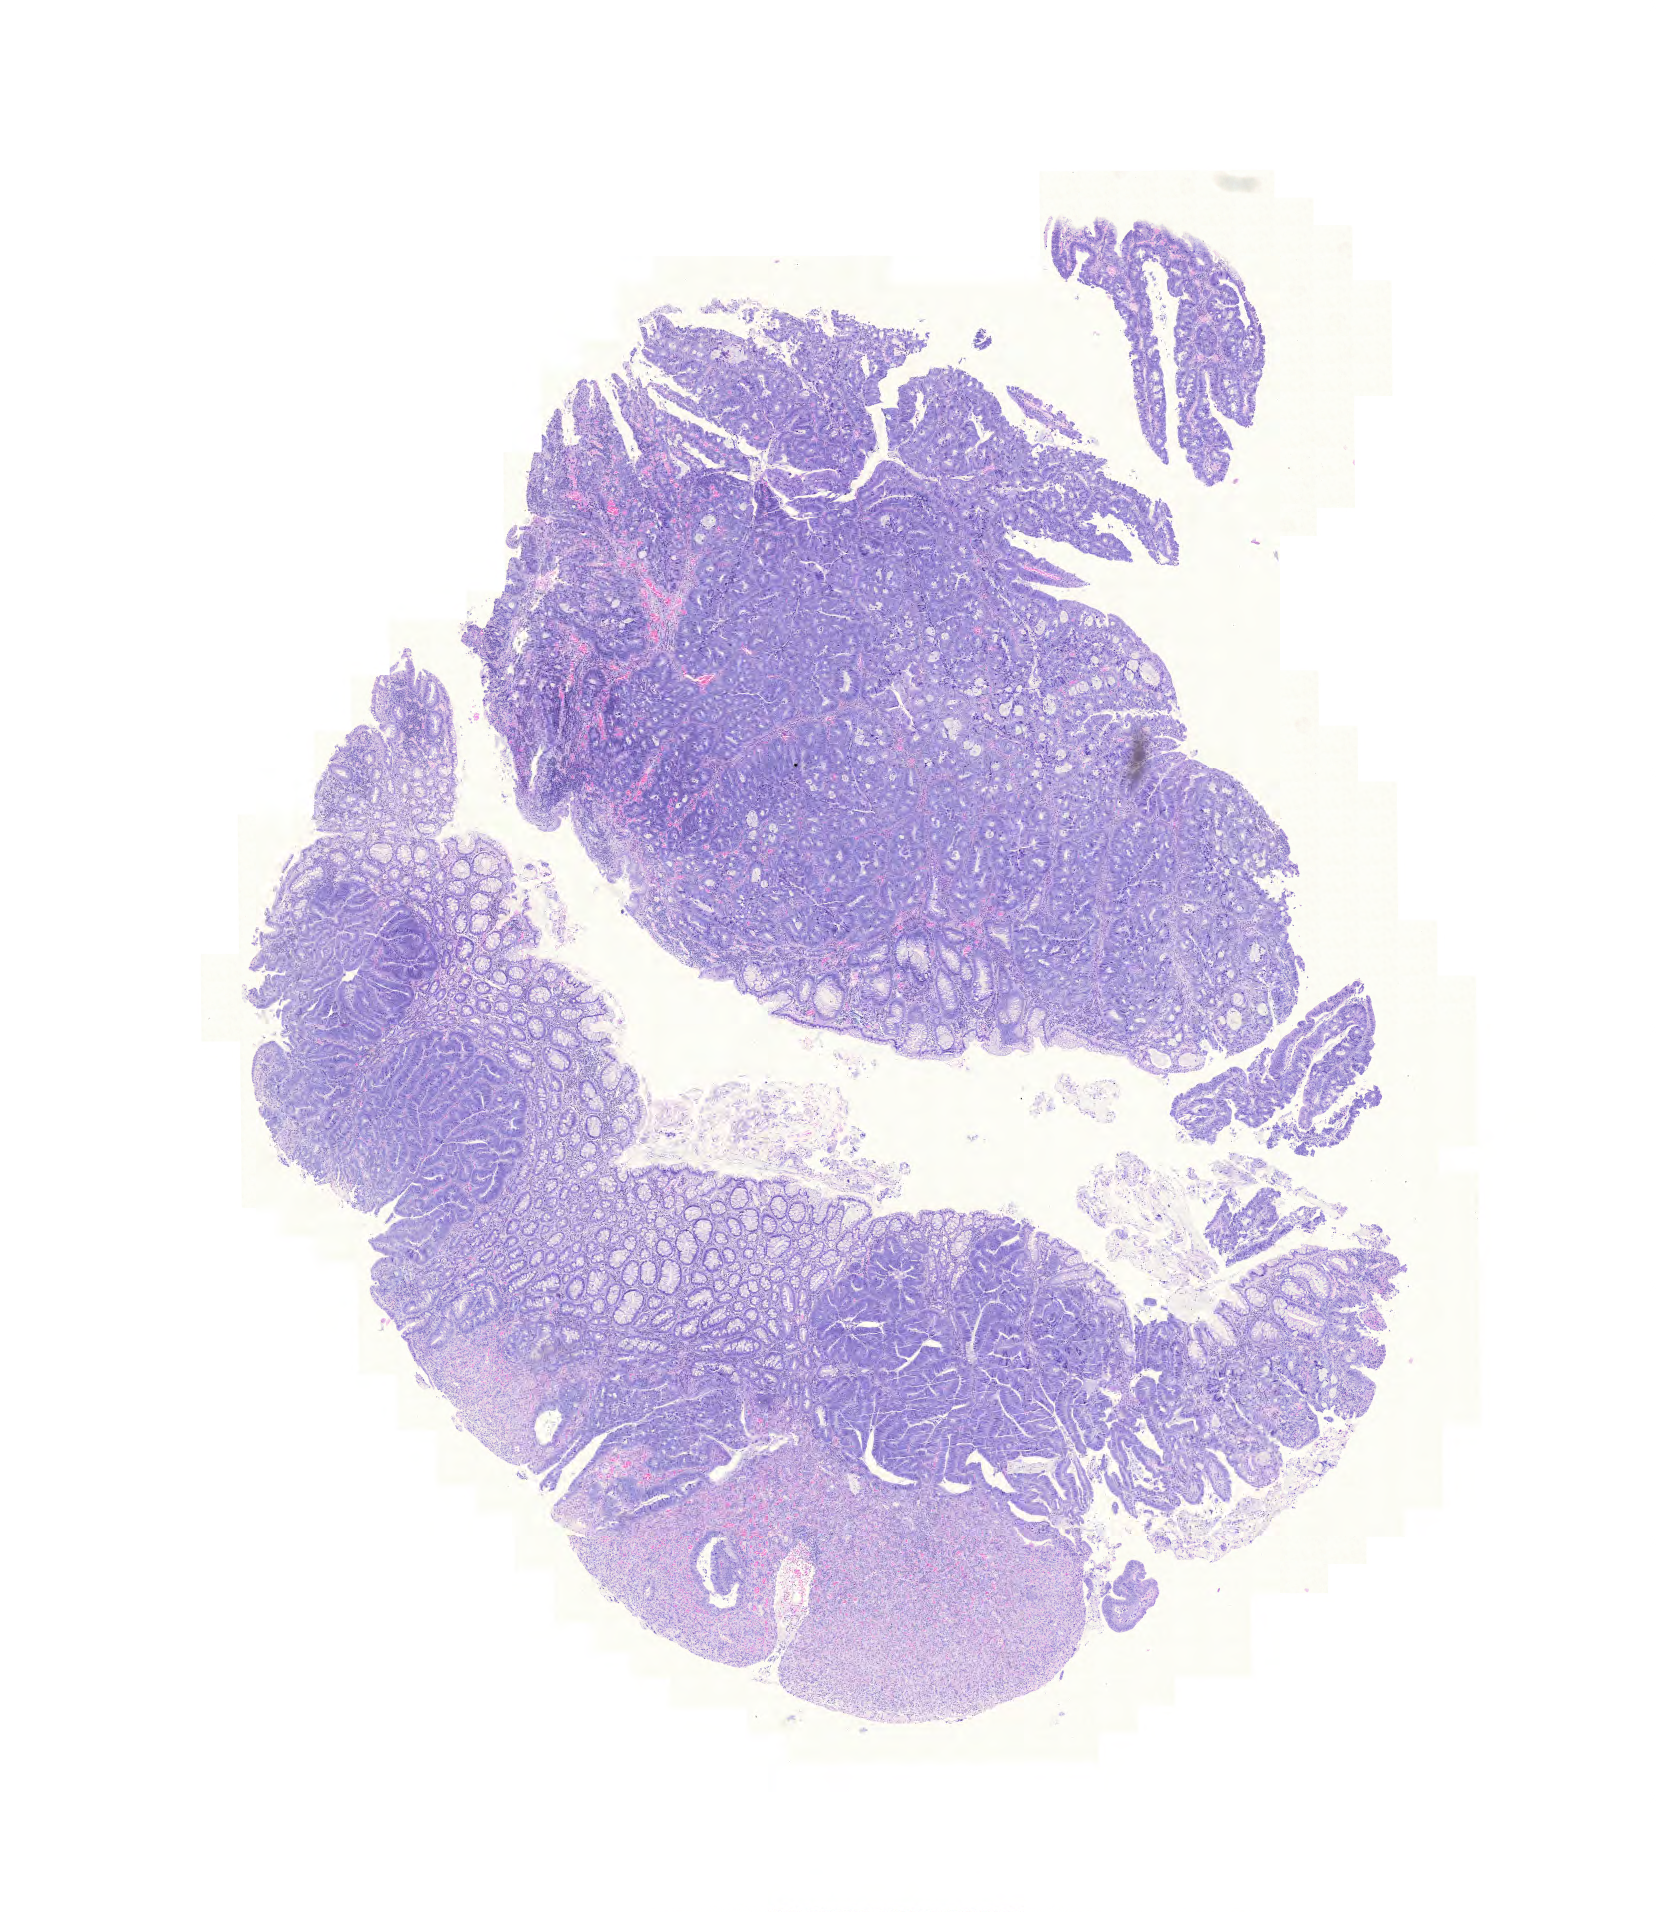
Digitized H&E-stained tissue section (whole slide), shown as a low-resolution overview of the whole scanned area (about 12.3 x 14.2 mm, slide scanned at 20x); FFPE section; sample: primary tumour, rectum. Male, age 66 years at initial diagnosis.
Pathologic diagnosis: Adenocarcinoma, NOS (rectosigmoid junction). AJCC pathologic stage: IV (6th edition).